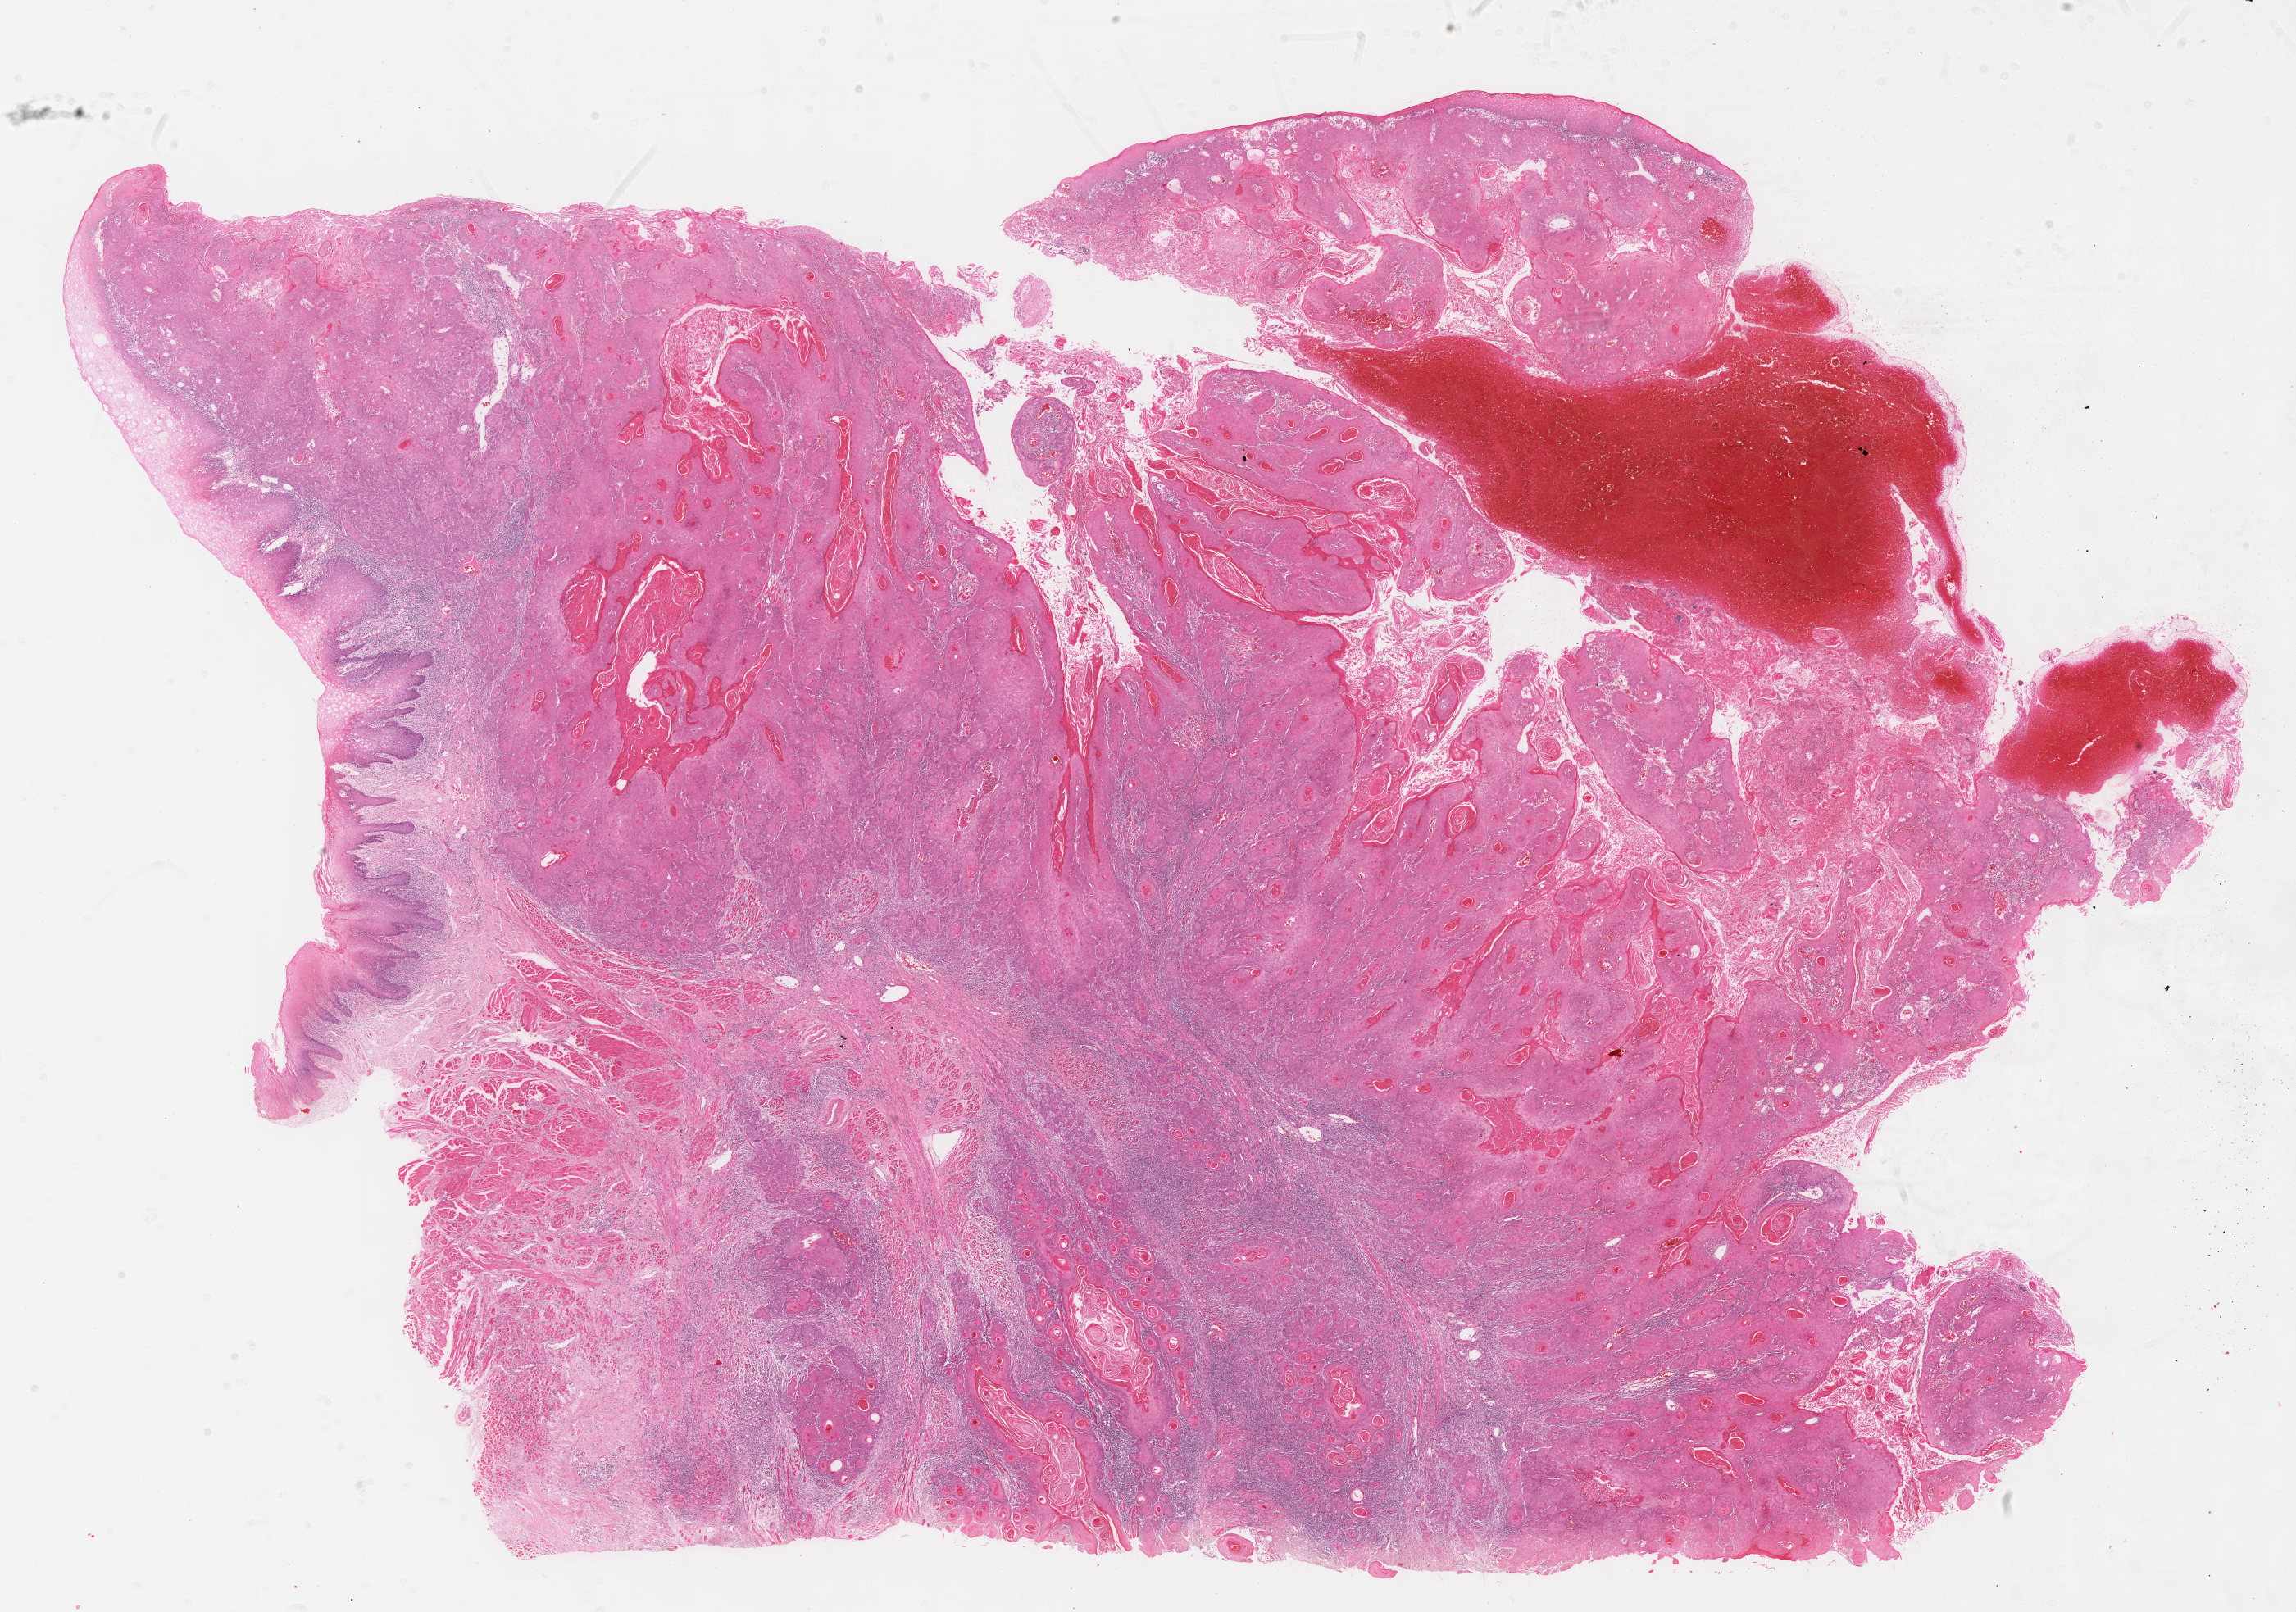
Whole-slide histology image, H&E-stained — low-resolution overview of the scanned area, about 22.6 x 15.9 mm (acquisition: 40x scan), formalin-fixed paraffin-embedded (FFPE) diagnostic section, sample: primary tumour, head and neck. Patient: female, age at initial diagnosis 65 years. Histologic grade: G1 (well differentiated).
• AJCC pathologic stage: IVA (7th edition)
• pathologic diagnosis: Squamous cell carcinoma, NOS (tongue, NOS)